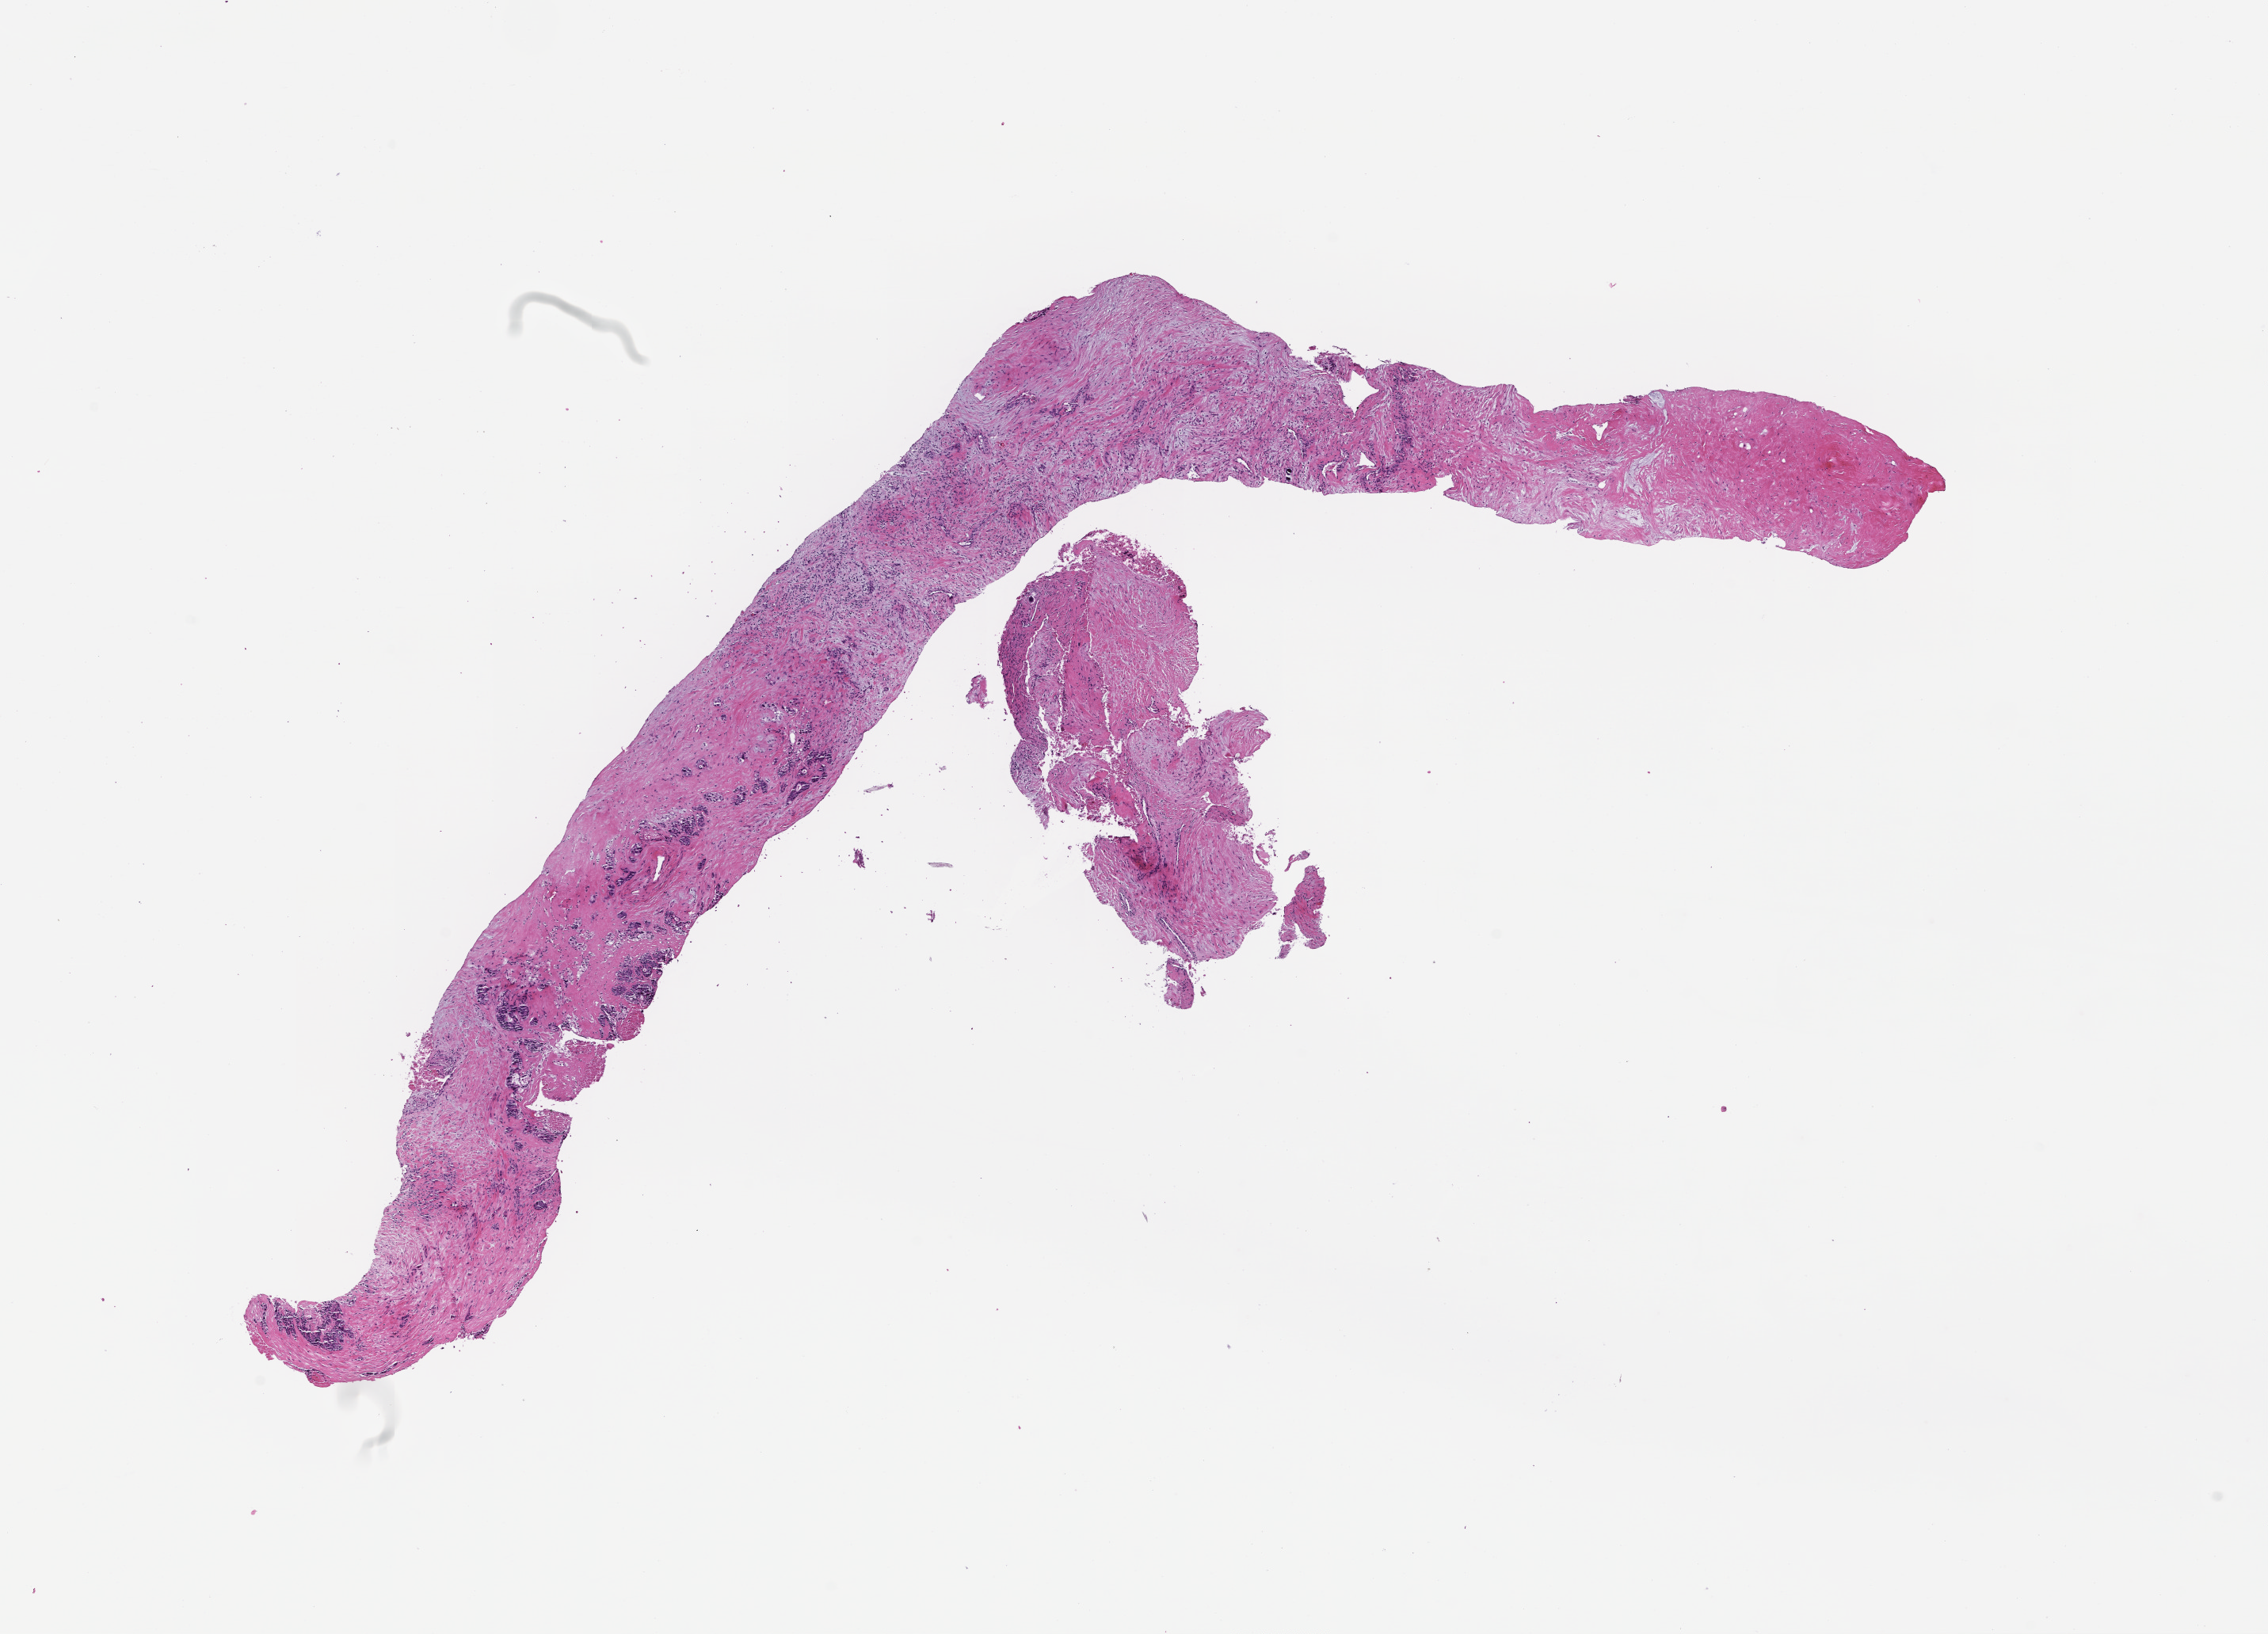
Digitized haematoxylin and eosin-stained section — shown as a low-resolution overview of the whole scanned area (about 11.6 x 8.3 mm), FFPE section. Patient sex: male.
This section: metastasis (sampled organ not recorded). Patient diagnosis (primary): Colorectal Carcinoma.